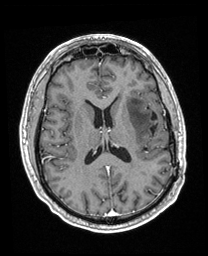
Brain MRI from a brain-tumour surgery series, one axial slice; slice 97 of 208 in the series (ordered by position); T1-weighted post-contrast; 1 mm slice thickness; 208 × 256 image matrix, field of view 211 × 260 mm. From the clinical record (not read from this slice): histopathology: Astrocytoma; WHO grade: 3; IDH mutation: yes; tumour location: Left Insular.
Structures marked on this image (manually delineated by an expert):
- previous resection cavity: bounding box [x1, y1, x2, y2] px = [150, 113, 158, 135]